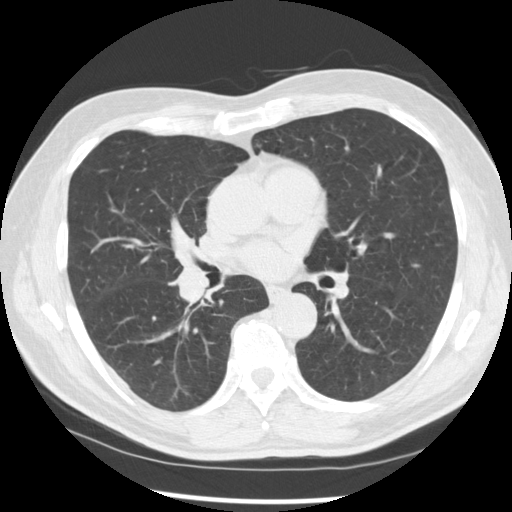
Low-dose screening chest CT, one axial slice. Position 149 of 277 along the scan axis. Reconstruction kernel STANDARD. 120 kVp. Lung window (W 1500 / L -600 HU). 2.5 mm slice thickness. 512 × 512 image matrix, field of view 365 × 365 mm.
Outlined on this slice (manually delineated by an expert):
- lesion 1 (tumor, middle lobe of right lung): box from (x=176, y=263) to (x=210, y=302) px